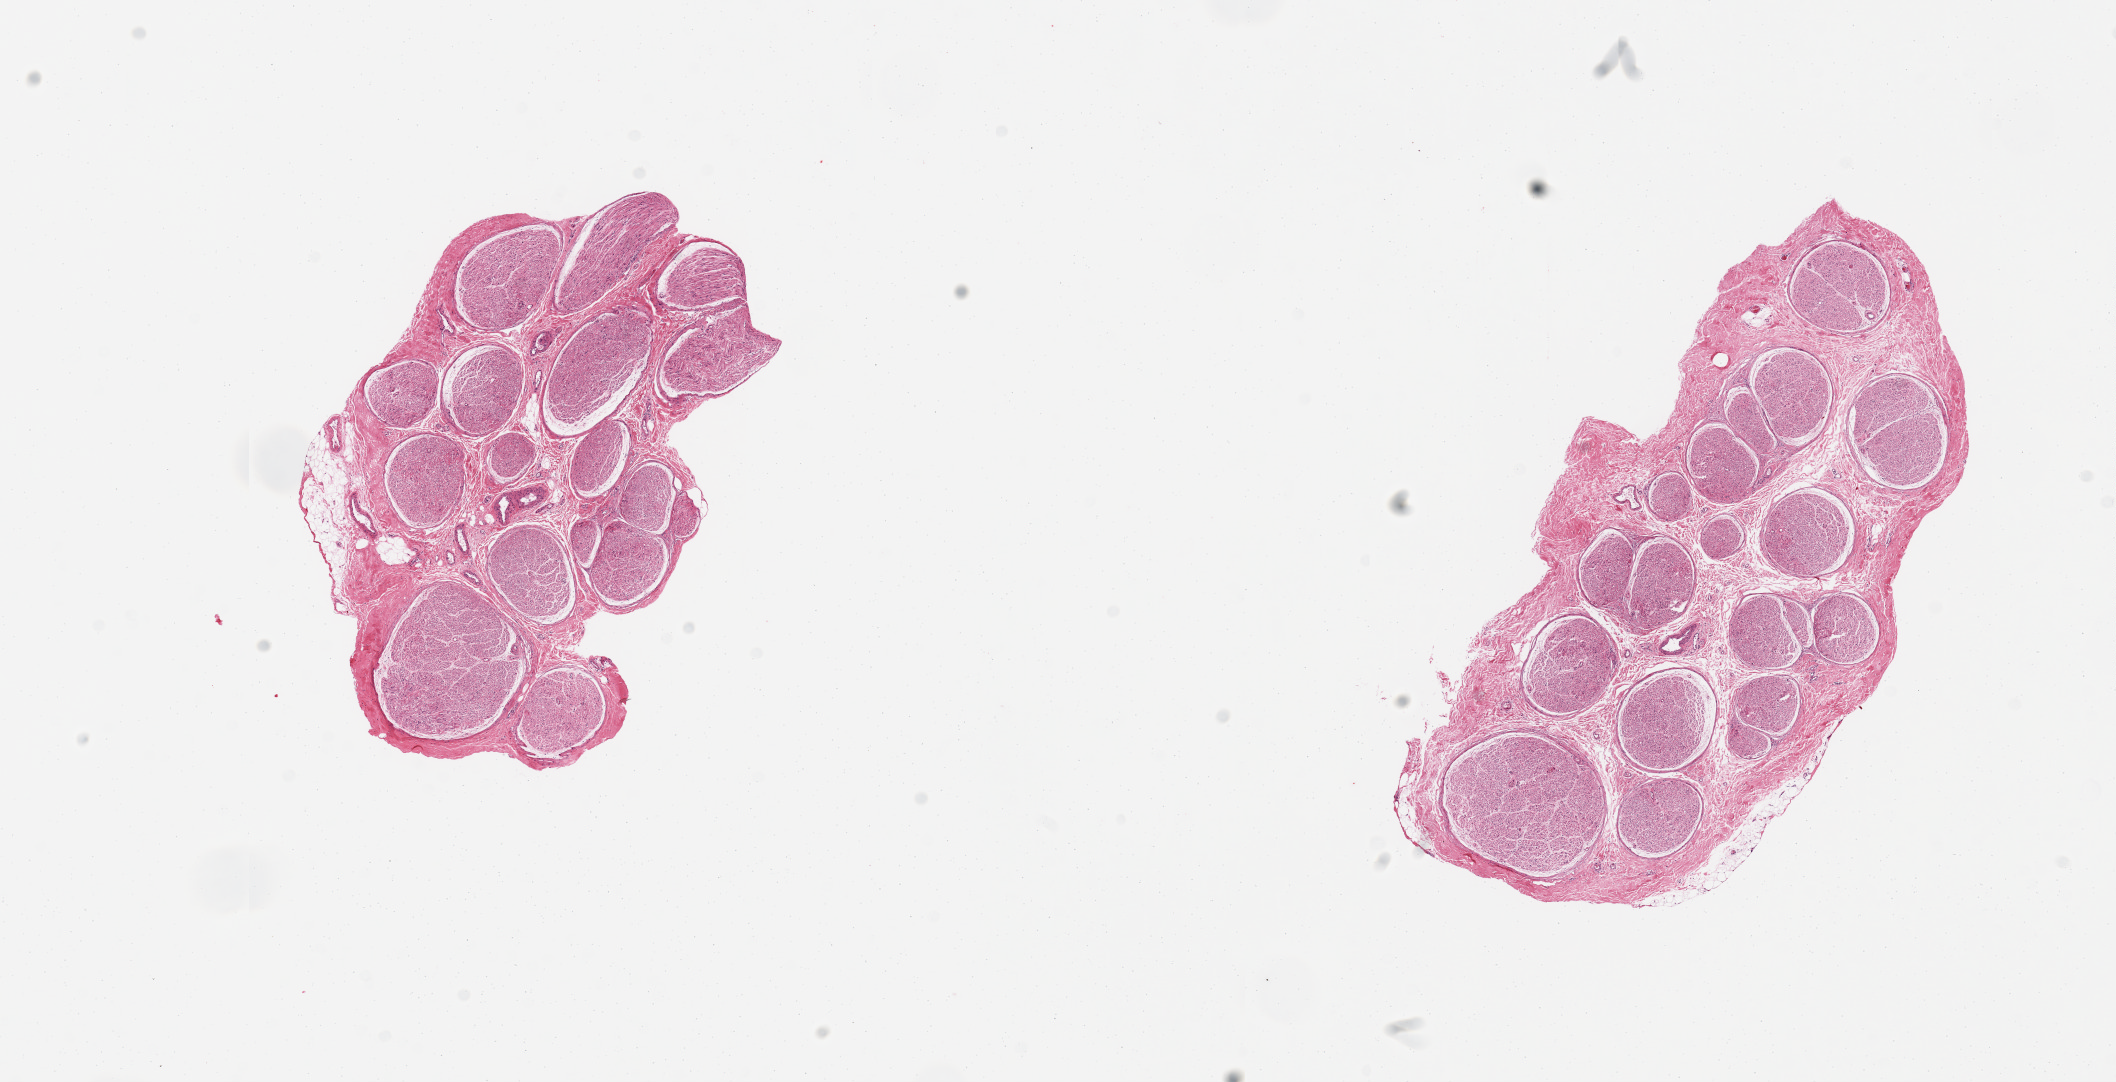
Whole-slide image, hematoxylin and eosin (H&E) stain, brightfield — shown as a low-resolution overview of the whole scanned area (about 16.7 x 8.6 mm). PAXgene-fixed, paraffin-embedded tissue. Sampled site (target tissue): tibial nerve. Tissue donor sample. Male donor.
Review note (as recorded): 2 pieces, only trace fat, good specimens.